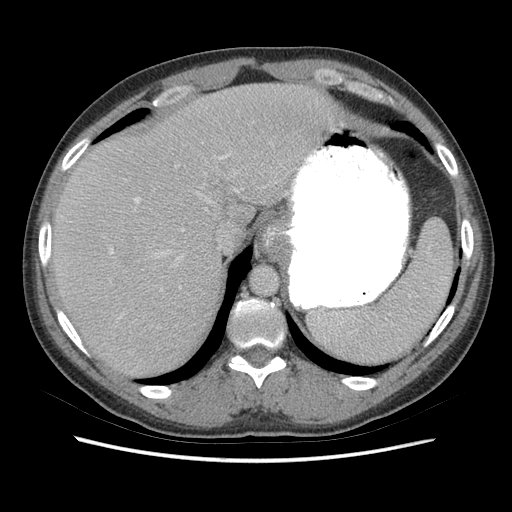
Contrast-enhanced abdominal CT (liver protocol), one axial slice. Slice 54 of 73 in the series (ordered by position). 140 kVp. Soft-tissue window (W 400 / L 40 HU). 512 × 512 image matrix, field of view 360 × 360 mm. Case-level facts recorded for this patient, not image findings: diagnosis: hepatocellular carcinoma (patient treated with transarterial chemoembolisation; whether this scan precedes or follows treatment is not stated here); TNM stage (as recorded): Stage-IIIA.
Outlined on this slice (semi-automatically segmented with operator editing):
- liver parenchyma outside the tumour (the mass and vessels are separate outlines, so this box may not span the whole liver): bounding box [x1, y1, x2, y2] px = [52, 82, 346, 376]
- liver vessels: [110, 154, 238, 318]